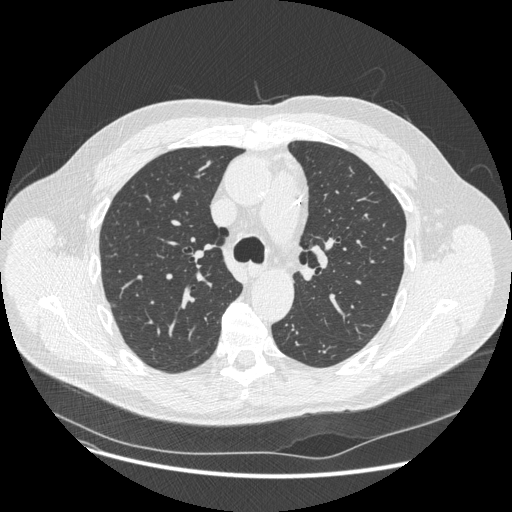
Low-dose screening chest CT, axial slice; second annual screen; lung window (W 1500 / L -600 HU); 1.25 mm slice thickness. Male, age 62 years at enrolment. Current smoker at enrolment.
Expert-annotated lung lesion, bounding box <100,292,128,318> (left, top, right, bottom; pixels). Reader record for this screening exam (exam-level; its link to the box is not recorded): non-calcified nodule or mass ≥4 mm, right upper lobe, 11 × 7 mm, smooth margins, pre-existing on the prior screen: yes. Lung cancer was diagnosed 482 days after this screen (after the third annual screen): adenocarcinoma, NOS, right upper lobe, moderately differentiated (G2), stage IA (AJCC 6th edition), 12 mm at pathology.